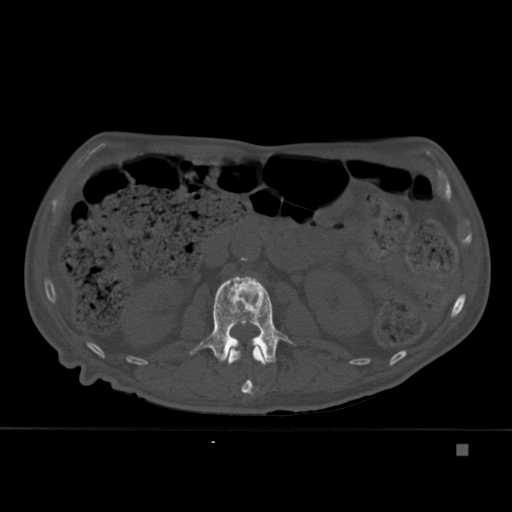
CT including the spine, one axial slice; slice 166 of 451 in the series (ordered by position); bone window (W 1800 / L 400 HU); 512 × 512 image matrix. Male patient, age 75 years. From the clinical record (not read from this slice): primary cancer: prostate.
Structures marked on this image (semi-automatically segmented with operator editing):
- L1 vertebra: box from (x=228, y=346) to (x=267, y=396) px
- L2 vertebra: (x=190, y=276)–(x=296, y=363)